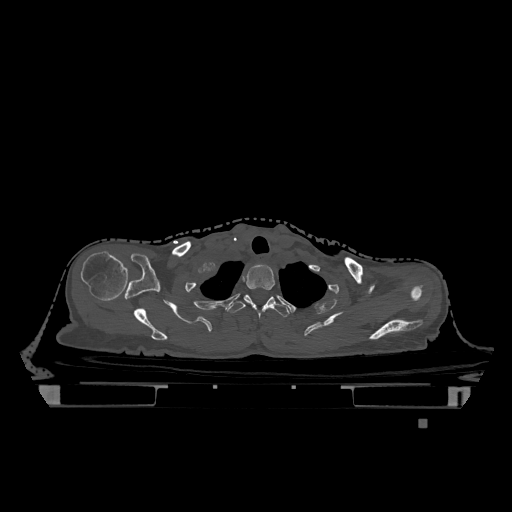
CT including the spine, one axial slice; slice 980 of 1317 in the series (ordered by position); bone window (W 1800 / L 400 HU); 0.5 mm slice thickness; 512 × 512 image matrix. Patient: female, 74 years. From the clinical record (not read from this slice): primary cancer: lung.
Structures marked on this image (semi-automatic segmentation, software-assisted and operator-edited):
- T1 vertebra: bounding box (x1, y1, x2, y2) in pixels: (244, 265, 275, 304)
- T2 vertebra: (227, 294, 290, 318)